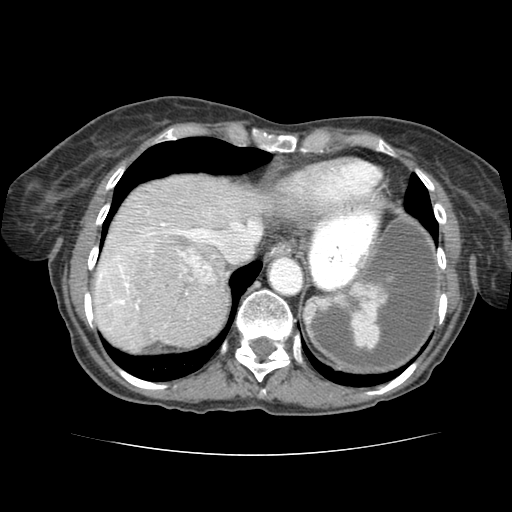
Contrast-enhanced abdominal CT (liver protocol), one axial slice; position 67 of 77 along the scan axis; reconstruction kernel STANDARD; 120 kVp; soft-tissue window (W 400 / L 40 HU); 2.5 mm slice thickness; 512 × 512 image matrix, field of view 340 × 340 mm. Case-level facts recorded for this patient, not image findings: diagnosis: hepatocellular carcinoma (patient treated with transarterial chemoembolisation; whether this scan precedes or follows treatment is not stated here); TNM stage (as recorded): Stage-I; Child-Pugh class: A; tumour differentiation: well differentiated; tumour size: 7.6 cm.
Structures marked on this image (semi-automatic segmentation, software-assisted and operator-edited):
- abdominal aorta: bounding box <269,256,301,294> (left, top, right, bottom; pixels)
- liver parenchyma outside the tumour (the mass and vessels are separate outlines, so this box may not span the whole liver): <92,172,287,340>
- mass: <136,243,220,341>
- liver vessels: <136,222,262,312>